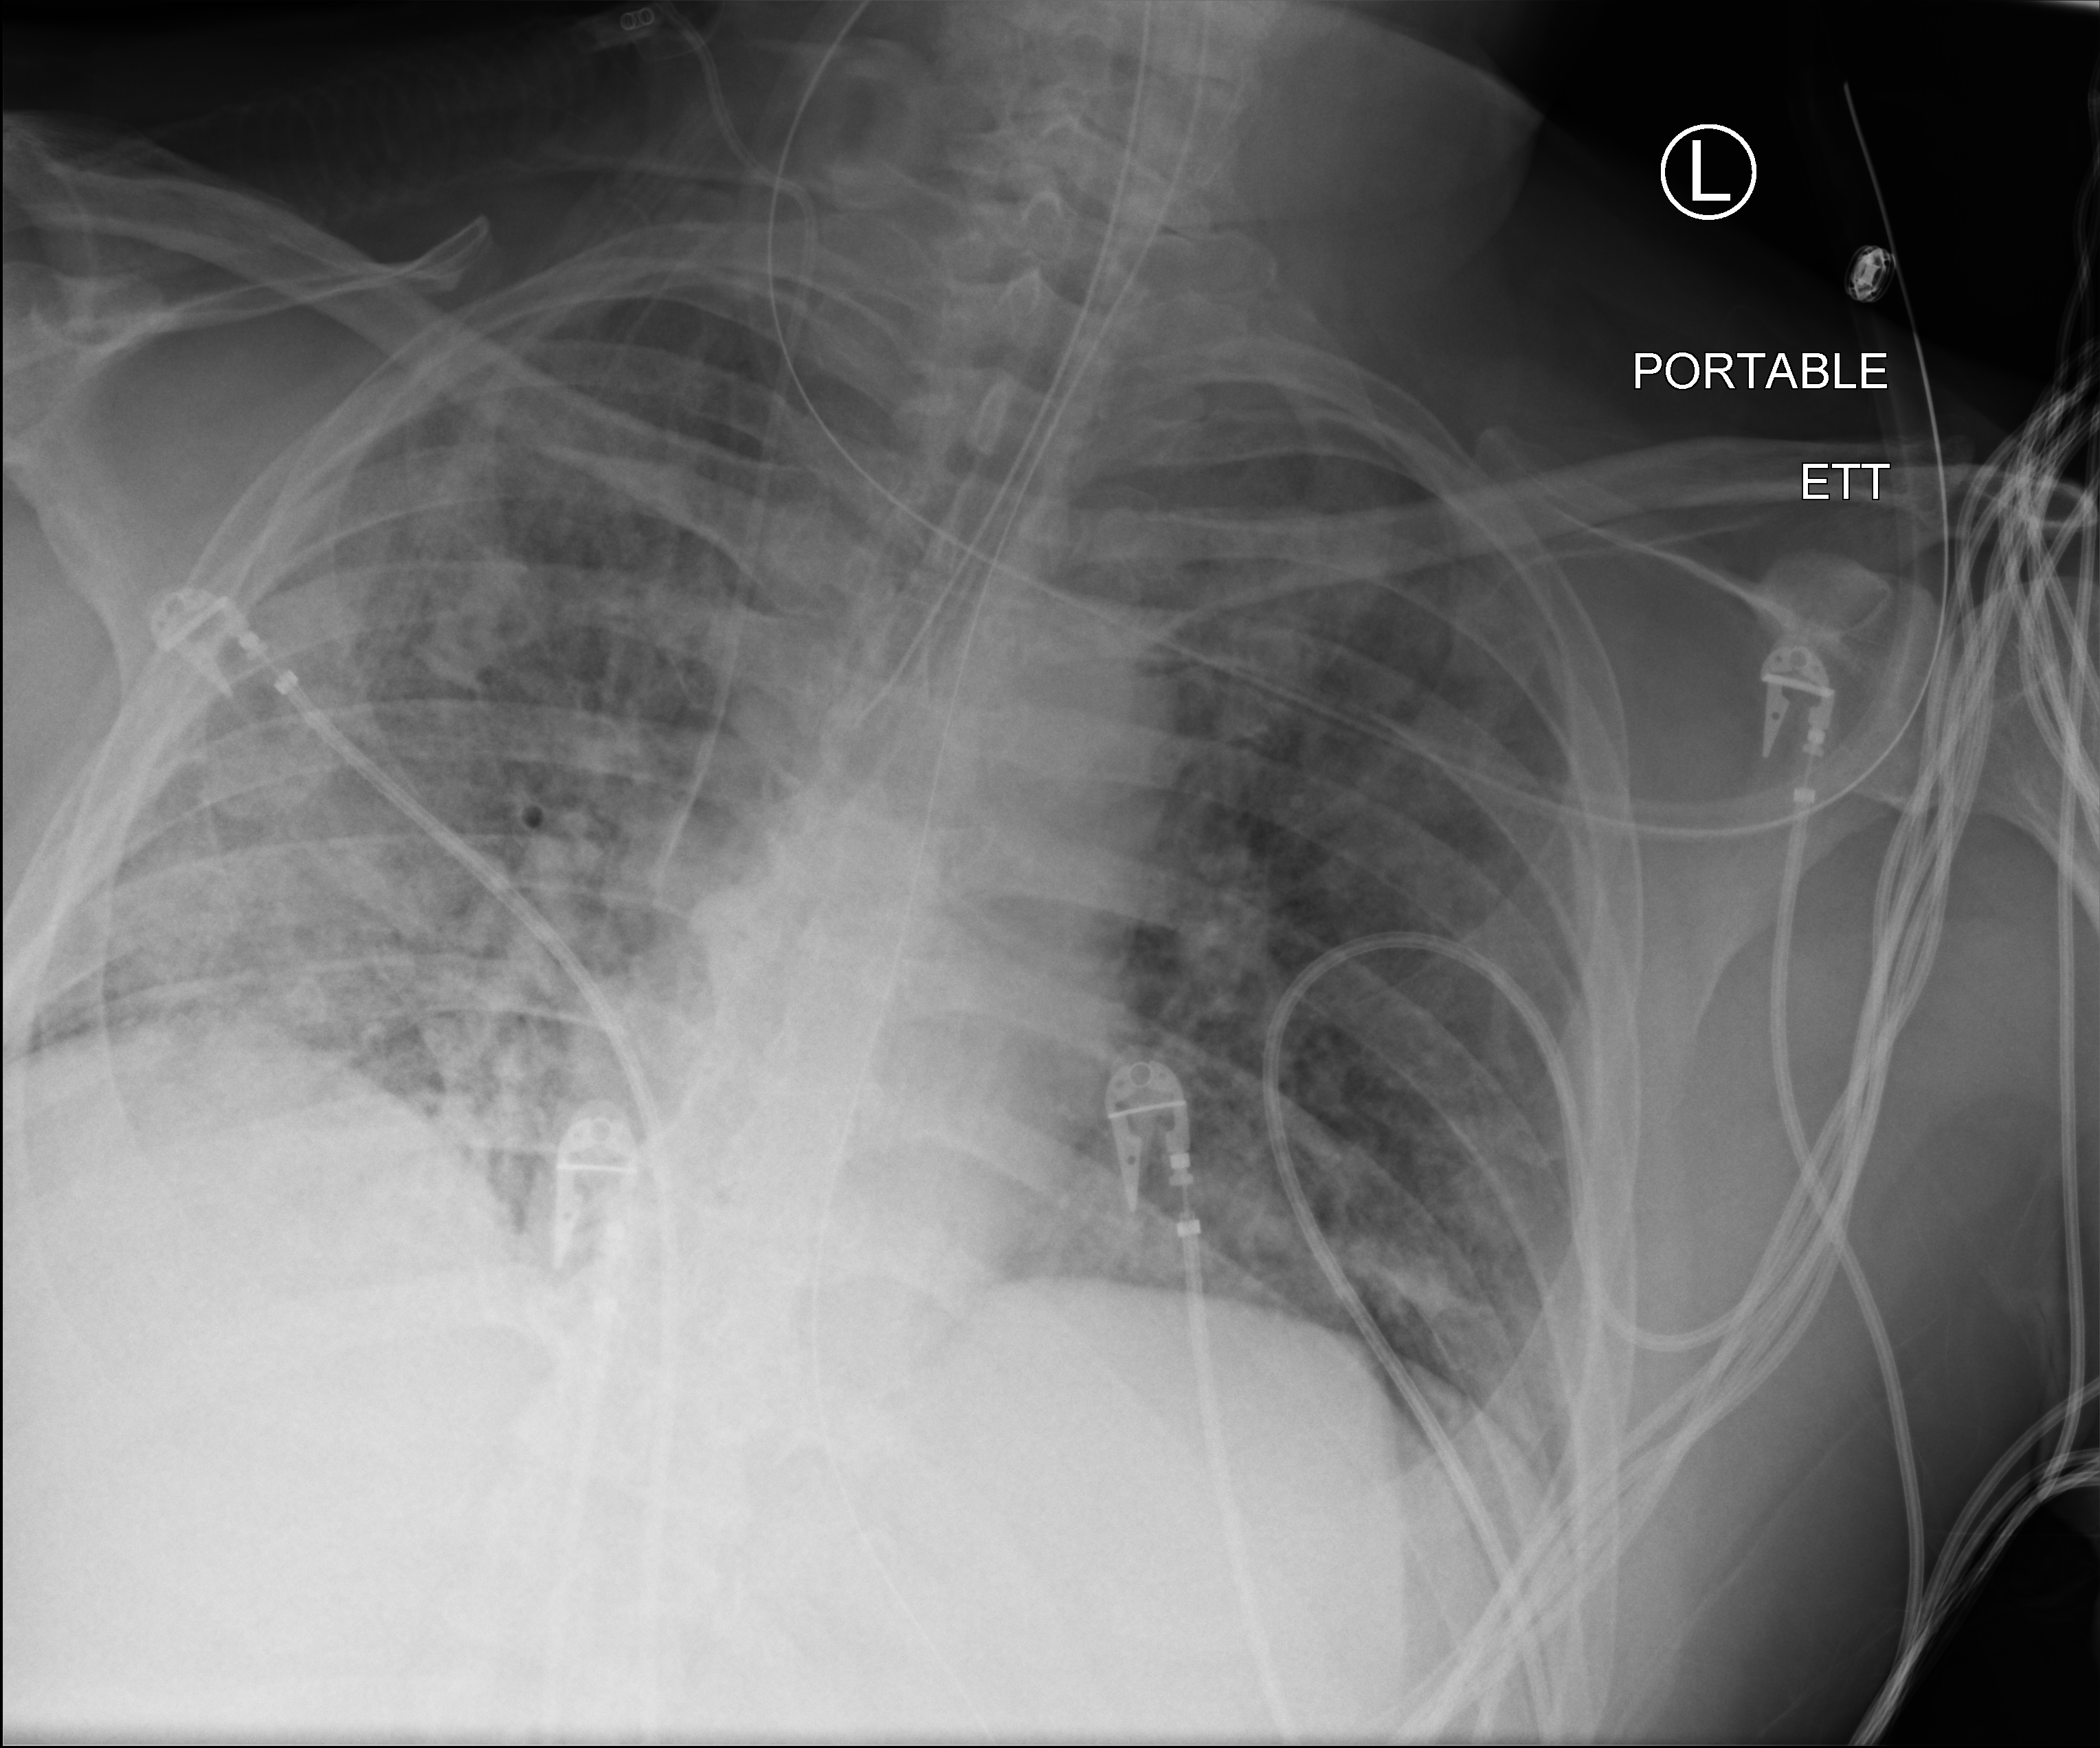
Portable chest radiograph; anteroposterior (AP) projection. Male patient hospitalised with COVID-19, age 60–74 years.
Admission-level facts for this patient (not findings on this image; timing relative to this image not recorded): COPD (admission record): no; mechanically ventilated during this hospital stay: yes; admitted to intensive care during this hospital stay: yes.